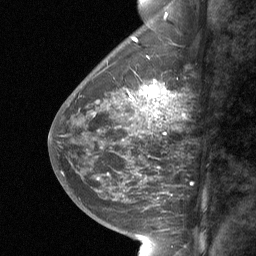
Breast MRI (dynamic contrast-enhanced), one sagittal slice; position 24 of 64 along the scan axis; dynamic contrast-enhanced study with each time point stored as its own series, time point 2 of 3 at this slice position (early post-contrast, ordered by acquisition time); 1.5 T; TE 4.8 ms, TR 27 ms; 2 mm slice thickness; 256 × 256 image matrix. Female patient, age 59 years. Case-level facts recorded for this patient, not image findings: setting: breast cancer imaged before/during neoadjuvant chemotherapy; receptor status: triple-negative.
Outlined on this slice (semi-automatically segmented with operator editing):
- analysis volume of interest (the breast-tissue region the enhancement analysis was run in; not a lesion): box from (x=138, y=71) to (x=158, y=122) px
- tumour enhancement mask (voxels above the 90 % enhancement threshold inside the analysis volume of interest): (x=145, y=80)–(x=156, y=97)